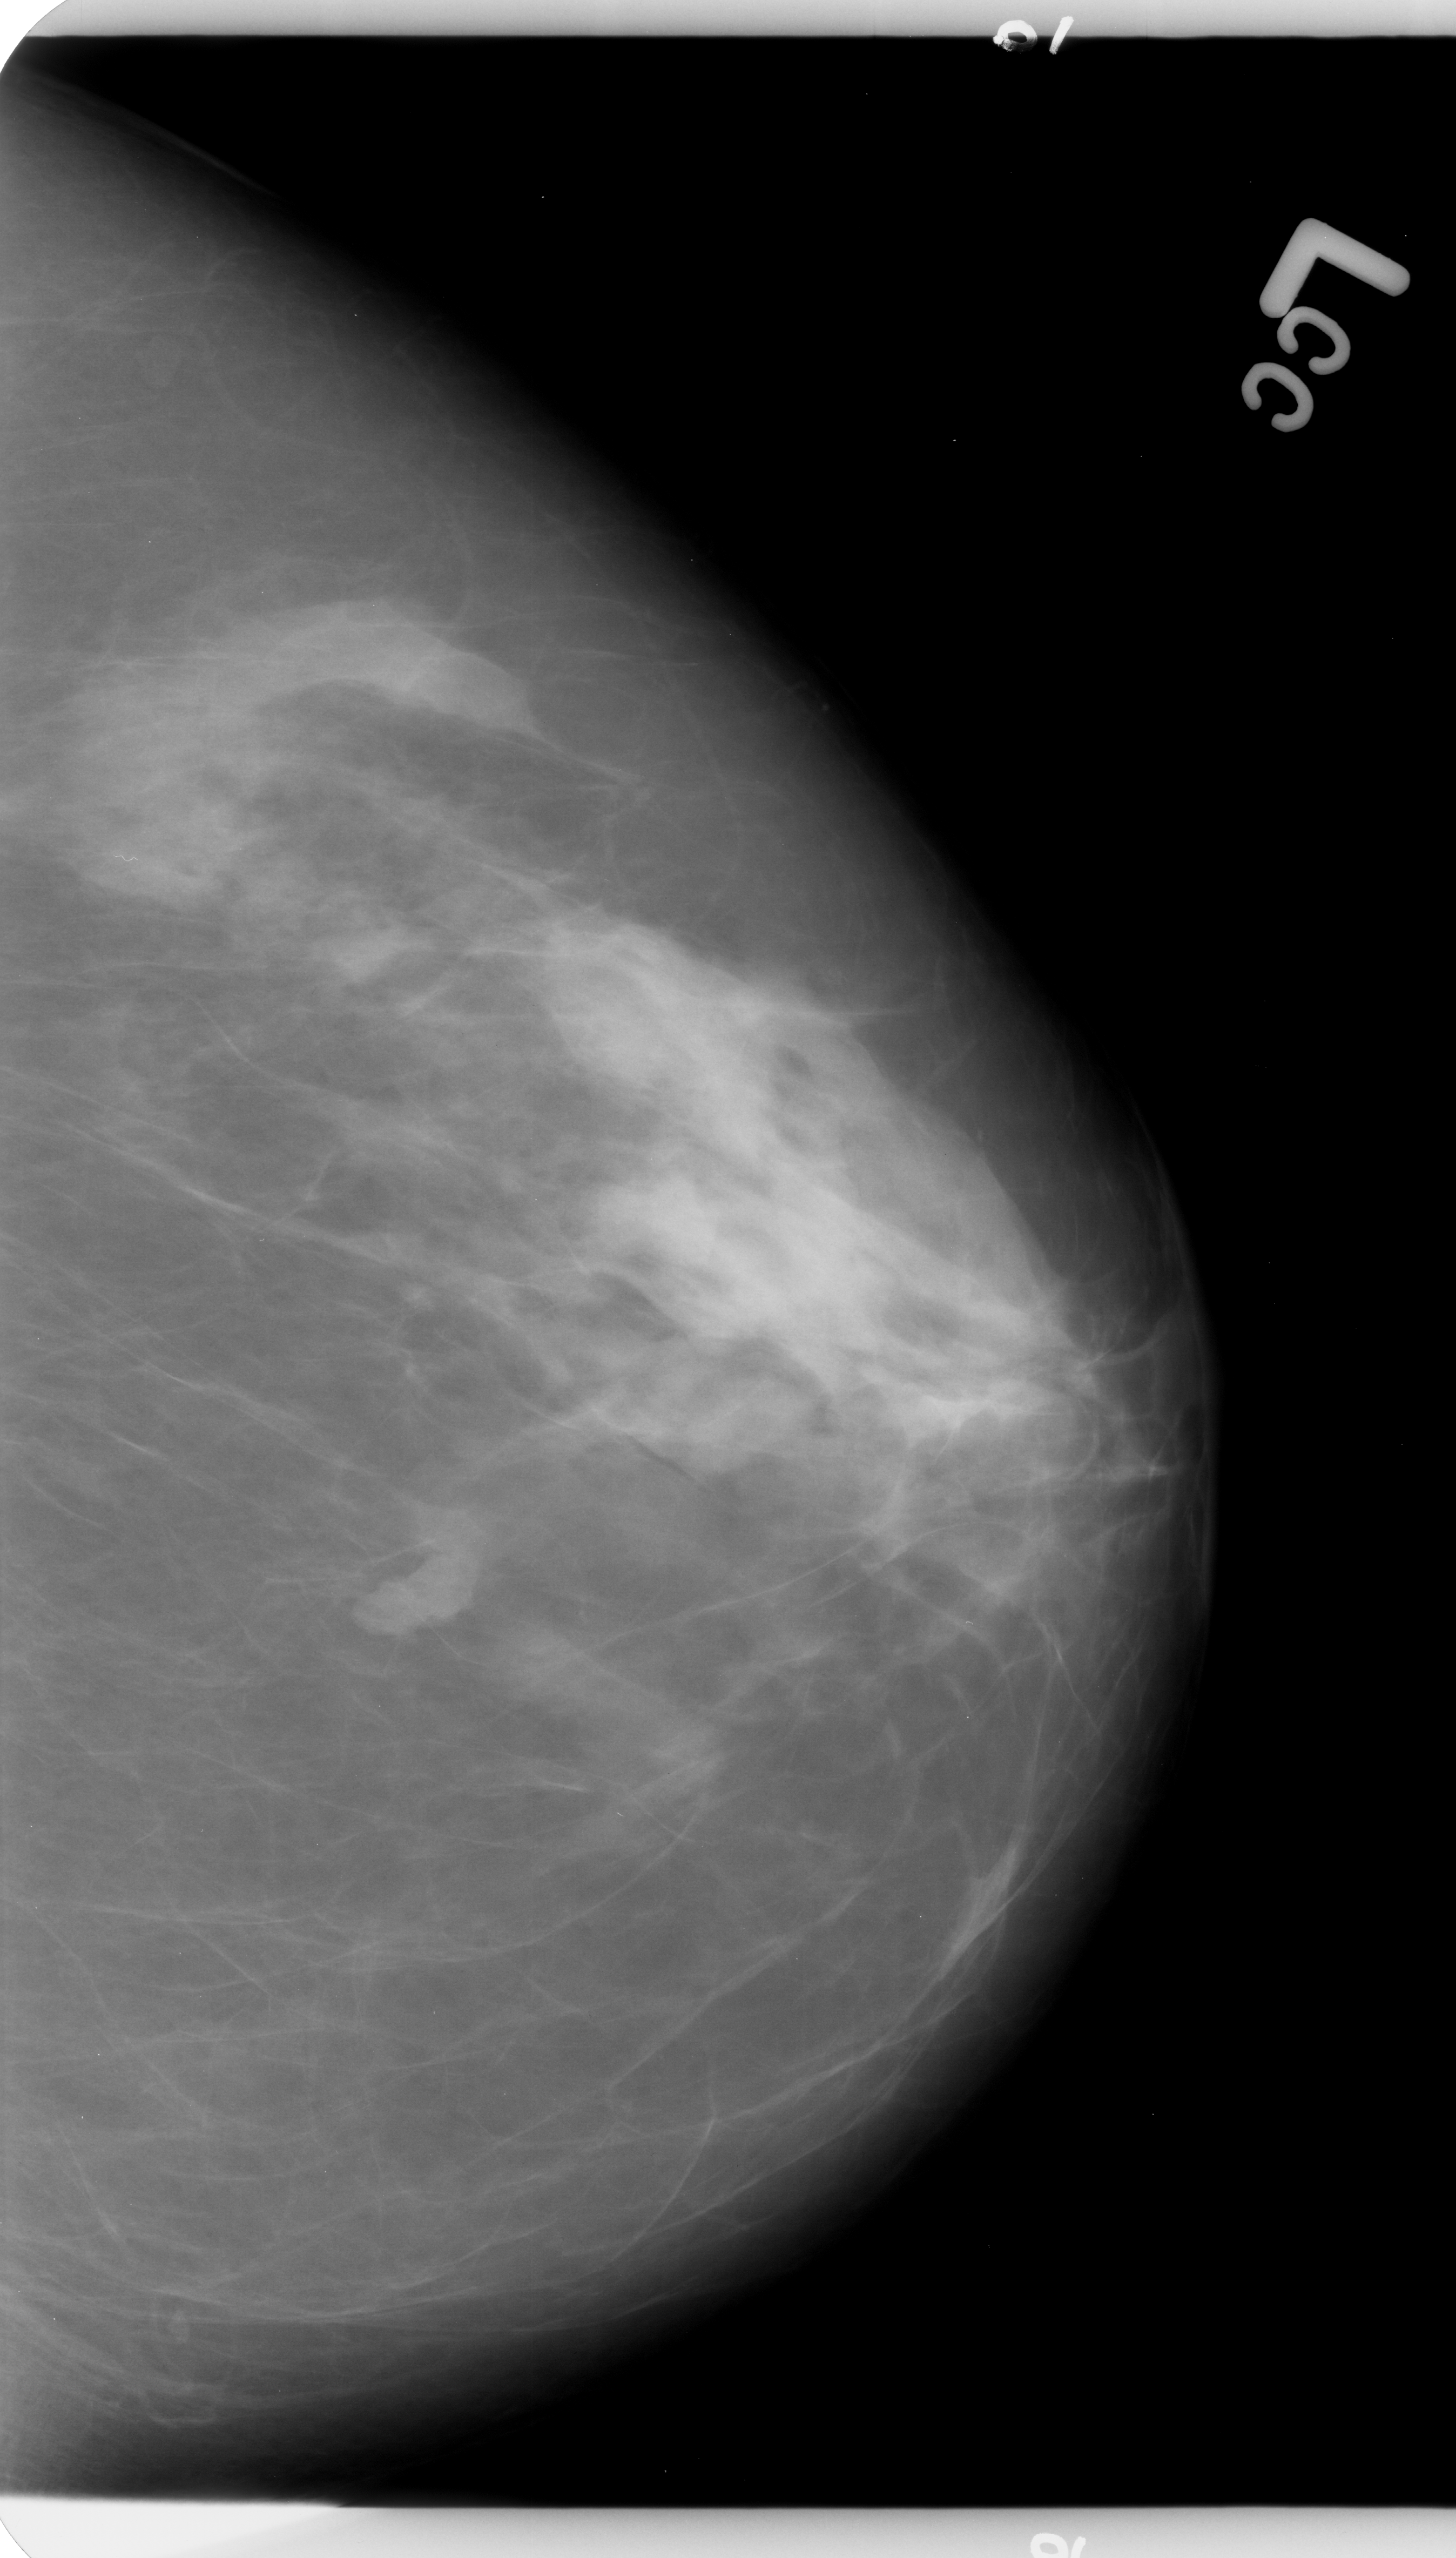
Digitized screen-film mammogram, left breast, craniocaudal (CC) view.
Finding: mass, shape lobulated, margins circumscribed / microlobulated; BI-RADS assessment category 4; subtlety rating 4 on a 1 (subtle) to 5 (obvious) scale; pathology (as recorded): benign.